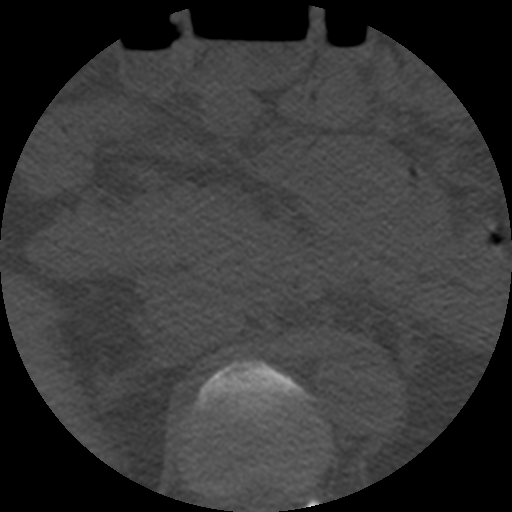
CT including the spine, one axial slice; position 227 of 508 along the scan axis; bone window (W 1800 / L 400 HU); 1.25 mm slice thickness; 512 × 512 image matrix, field of view 160 × 160 mm. Patient age 57 years. Case-level facts recorded for this patient, not image findings: primary cancer: prostate.
Outlined on this slice (semi-automatically segmented with operator editing):
- T11 vertebra: bounding box <287,470,315,490> (left, top, right, bottom; pixels)
- T12 vertebra: <189,360,316,504>